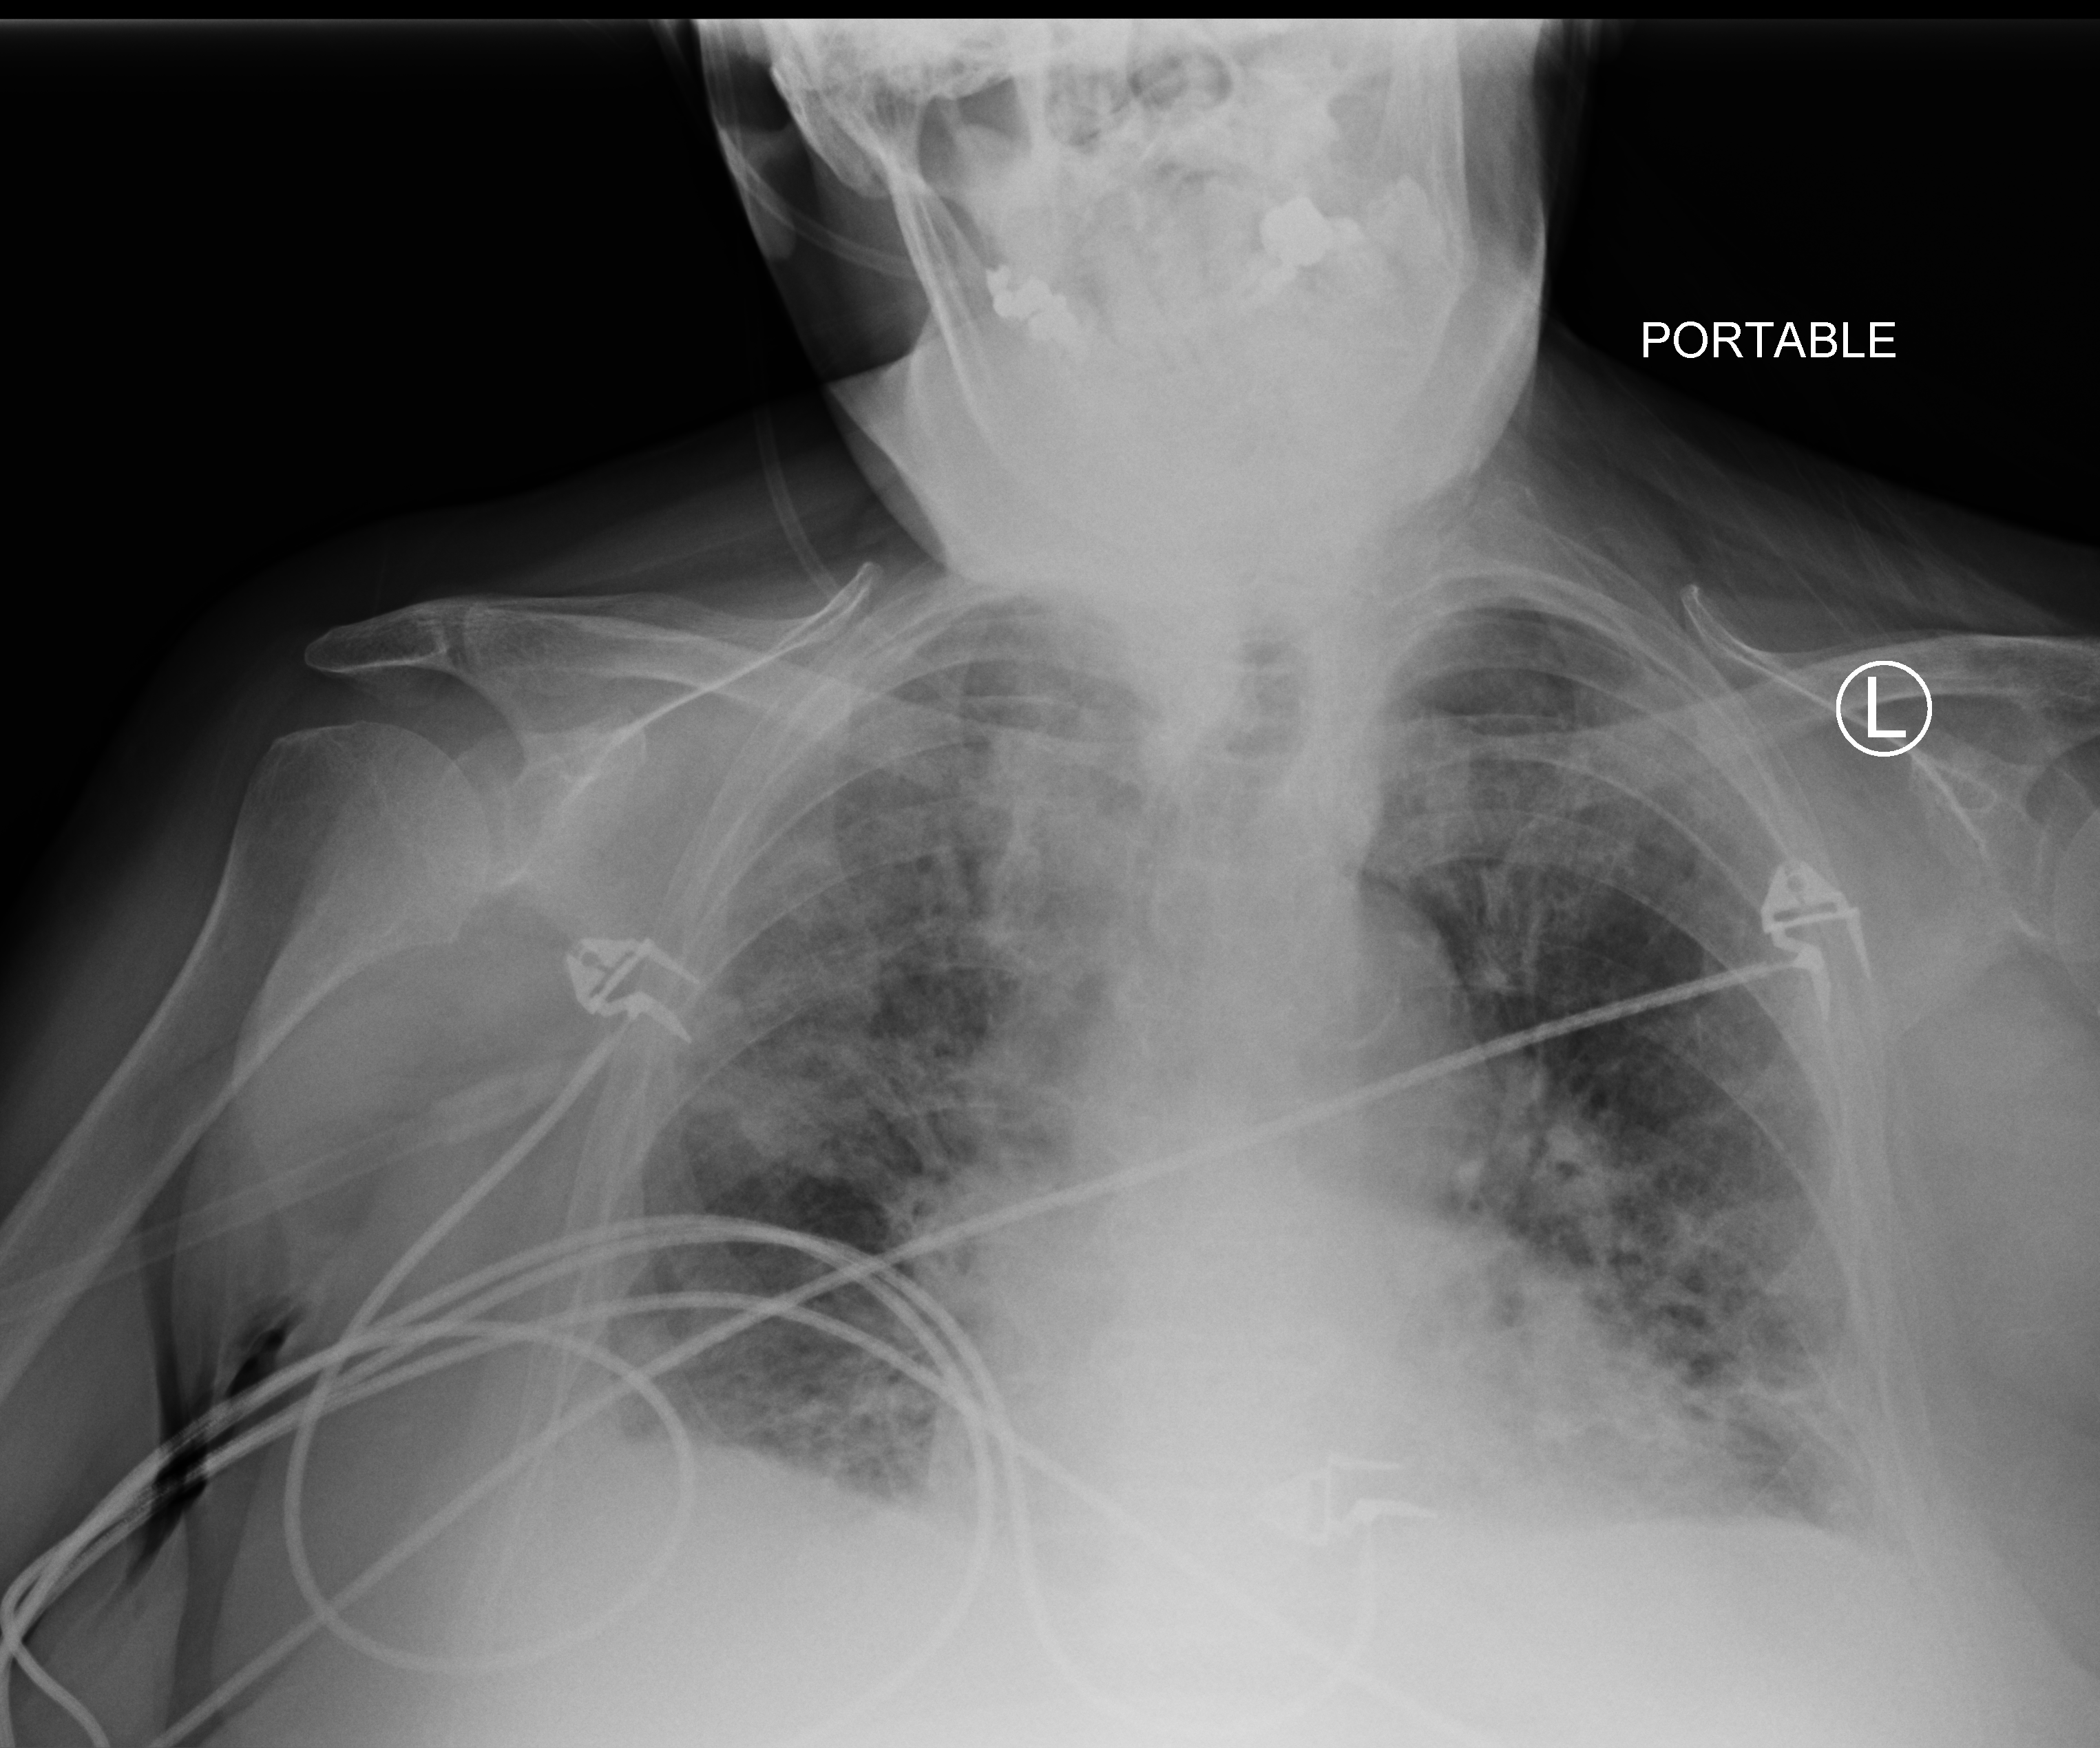
Bedside chest radiograph (computed radiography); anteroposterior (AP) projection. Patient hospitalised with COVID-19; female, aged 75–90 years.
From the hospital-stay record, not from the radiograph (when in the stay this image was taken is not recorded): COPD (admission record): no.